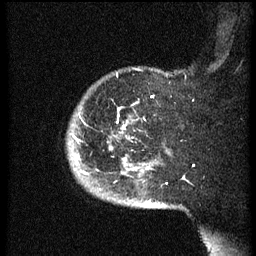
Breast MRI (dynamic contrast-enhanced), one sagittal slice; position 51 of 60 along the scan axis; dynamic contrast-enhanced series, image 2 of 3 at this slice position (ordered by acquisition); 1.5 T; TE 4.2 ms, TR 8.4 ms; 2.5 mm slice thickness; 256 × 256 image matrix, field of view 200 × 200 mm. Female patient, age 38 years. From the clinical record (not read from this slice): setting: breast cancer imaged before/during neoadjuvant chemotherapy; receptor status: HER2-positive.
Annotated regions visible in this slice (semi-automatically segmented with operator editing):
- analysis volume of interest (the breast-tissue region the enhancement analysis was run in; not a lesion): box from (x=68, y=74) to (x=171, y=202) px
- tumour enhancement mask (voxels above the 70 % enhancement threshold inside the analysis volume of interest): (x=74, y=126)–(x=151, y=175)